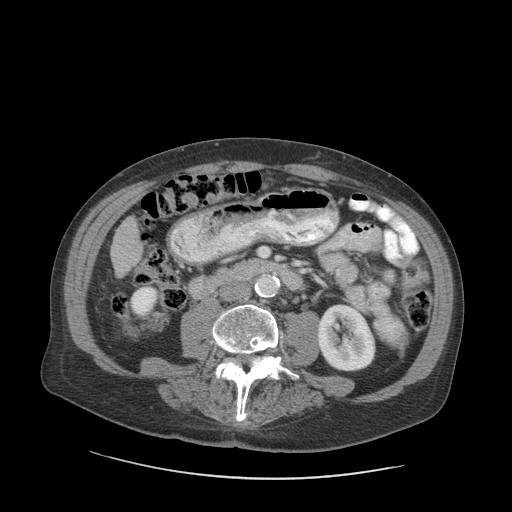
Contrast-enhanced abdominal CT (liver protocol), one axial slice; slice 21 of 89 in the series (ordered by position); reconstruction kernel STANDARD; 140 kVp; soft-tissue window (W 400 / L 40 HU); 2.5 mm slice thickness; 512 × 512 image matrix, field of view 420 × 420 mm. Case-level facts recorded for this patient, not image findings: diagnosis: hepatocellular carcinoma (patient treated with transarterial chemoembolisation; whether this scan precedes or follows treatment is not stated here); TNM stage (as recorded): Stage-I; Child-Pugh class: A.
Structures marked on this image (semi-automatically segmented with operator editing):
- liver parenchyma outside the tumour (the mass and vessels are separate outlines, so this box may not span the whole liver): bounding box (x1, y1, x2, y2) in pixels: (110, 216, 142, 276)